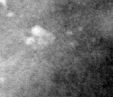
Cropped region of a digitized screen-film mammogram centred on a radiologist-marked abnormality; right breast; CC view; BI-RADS breast density category 3 (scale 1–4).
- Calcifications, morphology pleomorphic, distribution clustered; BI-RADS assessment category 4; pathology result (as recorded, not read from the image): malignant.